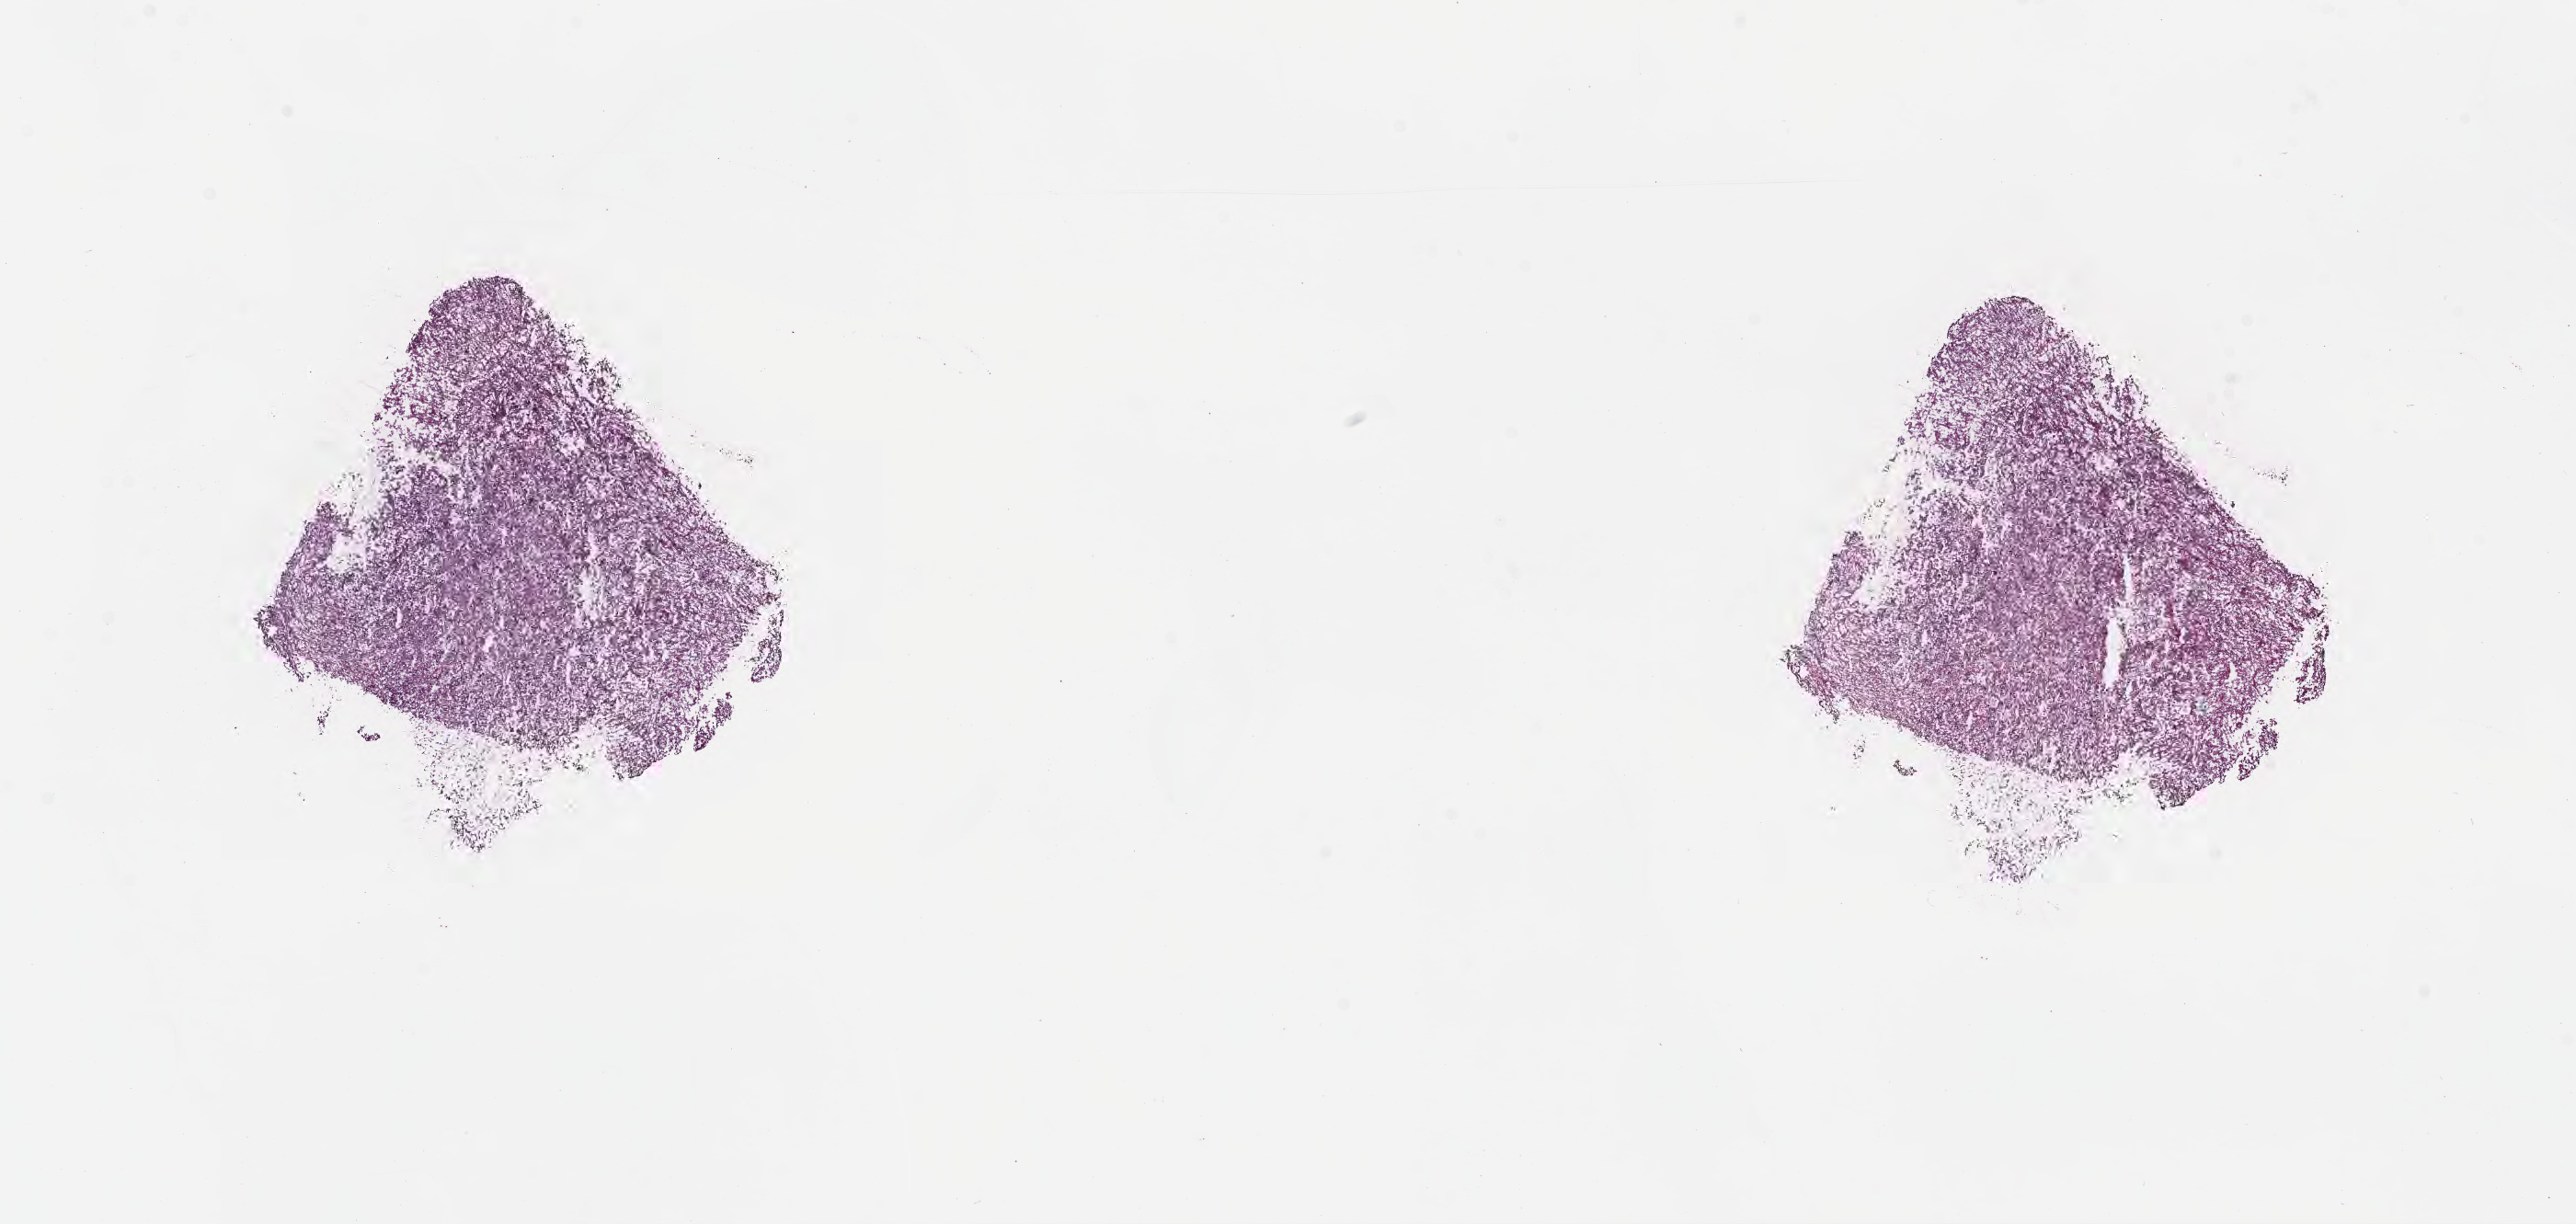
Whole-slide image, H&E stain — shown as a low-resolution overview of the whole scanned area (about 22.7 x 10.8 mm). Cryosection. Specimen: metastatic tumor tissue, resected from lymph node. Patient: male, age at initial diagnosis 69 years. Slide review estimates, as recorded: tumor cells 67%, tumor nuclei 73%, stromal cells 8%, necrosis 0%, normal cells 25%. Infiltration values recorded for this section: lymphocyte infiltration 2%, monocyte infiltration 4%, neutrophil infiltration 0%.
Patient diagnosis (primary): Malignant melanoma, NOS. Section: top of the tissue portion.